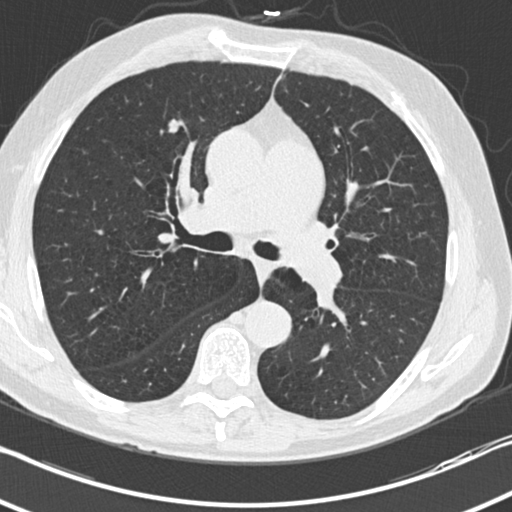
Axial slice from a low-dose chest CT screening exam; third annual screen; lung window (W 1500 / L -600 HU); 2 mm slice thickness; standard (soft-tissue) reconstruction kernel (B30f); slice 86 of 212 in the series. Male, age 70 years at enrolment. Current smoker at enrolment.
- Lesion marked by an expert reader, bounding box <157,106,200,143> (left, top, right, bottom; pixels).
- Screening reader's record for this exam (one nodule recorded; not confirmed to be the boxed lesion): non-calcified nodule or mass ≥4 mm, right middle lobe, 9 × 8 mm, smooth margins, soft tissue attenuation, pre-existing on the prior screen: no.
- Official screen result: positive, other.
- Participant outcome: lung cancer diagnosed 53 days after this screen — squamous cell carcinoma, NOS, right upper lobe, moderately differentiated (G2), stage IA (AJCC 6th edition), 10 mm at pathology.